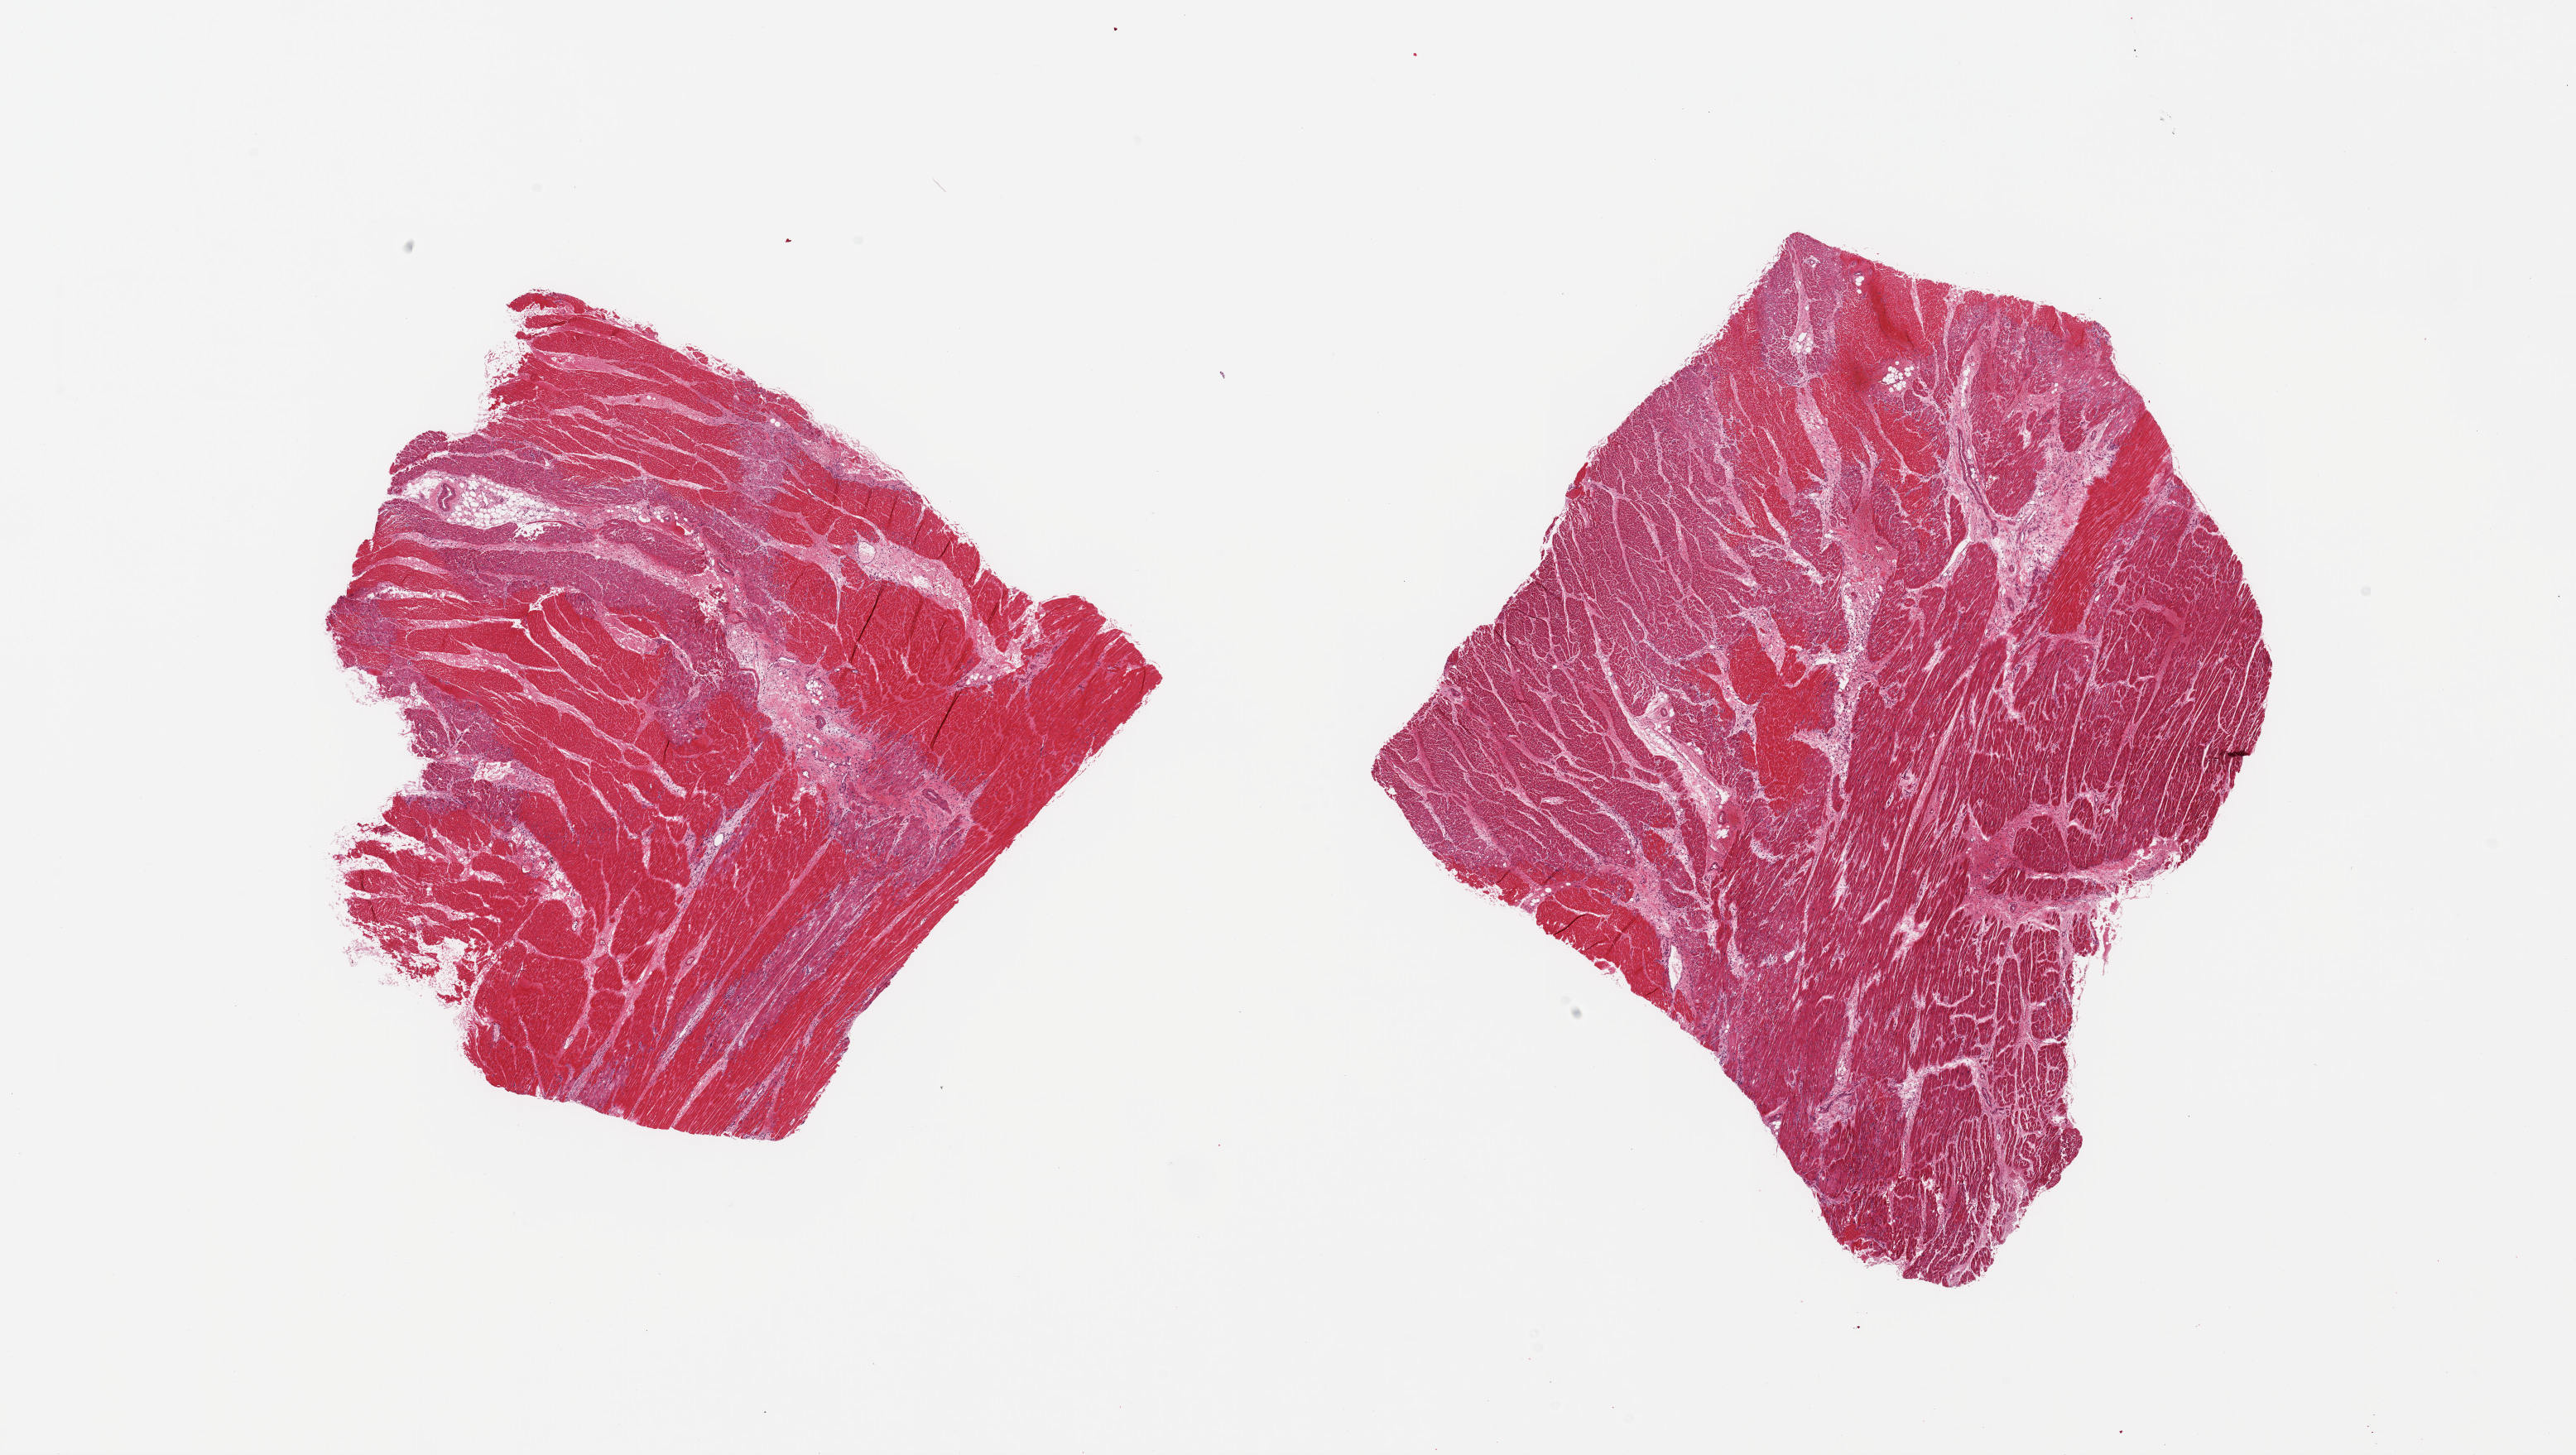
Digitized hematoxylin and eosin (H&E)-stained section, brightfield, whole scanned area (about 24.6 x 13.9 mm, from a 20x scan) shown as a low-resolution overview; PAXgene-fixed, paraffin-embedded tissue; target tissue: heart; donor tissue sample. Donor sex: male.
- review note (as recorded): 2 pieces, ~40% involved by subacute infarction